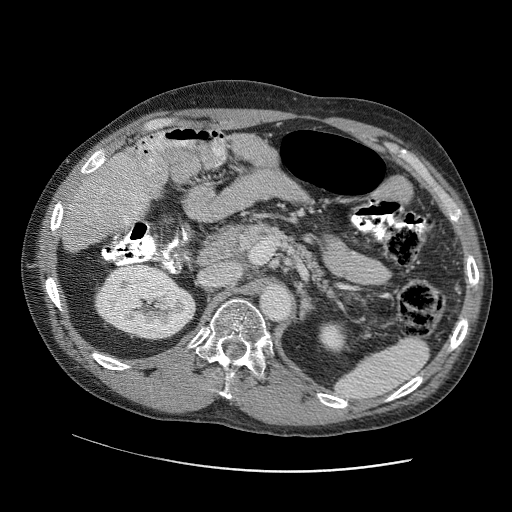
Contrast-enhanced abdominal CT (liver protocol), one axial slice; position 54 of 109 along the scan axis; reconstruction kernel STANDARD; 120 kVp; soft-tissue window (W 400 / L 40 HU); 512 × 512 image matrix, field of view 400 × 400 mm. Case-level facts recorded for this patient, not image findings: diagnosis: hepatocellular carcinoma (patient treated with transarterial chemoembolisation; whether this scan precedes or follows treatment is not stated here); TNM stage (as recorded): Stage-IIIC; Child-Pugh class: B; tumour differentiation: well differentiated; tumour nodularity: uninodular.
Annotated regions visible in this slice (semi-automatic segmentation, software-assisted and operator-edited):
- liver parenchyma outside the tumour (the mass and vessels are separate outlines, so this box may not span the whole liver): box from (x=104, y=138) to (x=198, y=200) px
- liver vessels: (x=125, y=140)–(x=195, y=188)